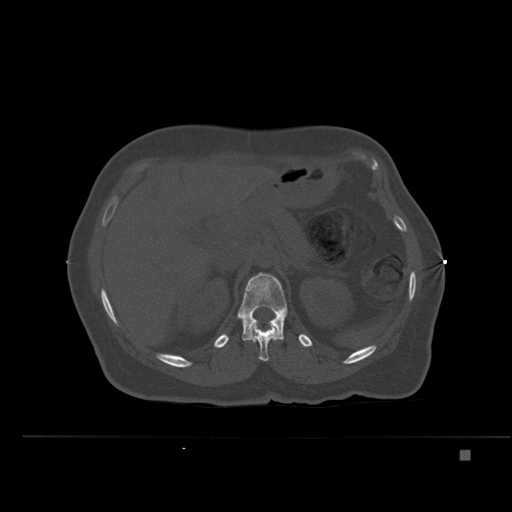
CT including the spine, one axial slice; position 243 of 477 along the scan axis; bone window (W 1800 / L 400 HU); 1.5 mm slice thickness; 512 × 512 image matrix. Female patient, age 74 years. From the clinical record (not read from this slice): primary cancer: colon.
Structures marked on this image (semi-automatically segmented with operator editing):
- L1 vertebra: bounding box (x1, y1, x2, y2) in pixels: (237, 273, 287, 341)
- T12 vertebra: (250, 324, 278, 362)